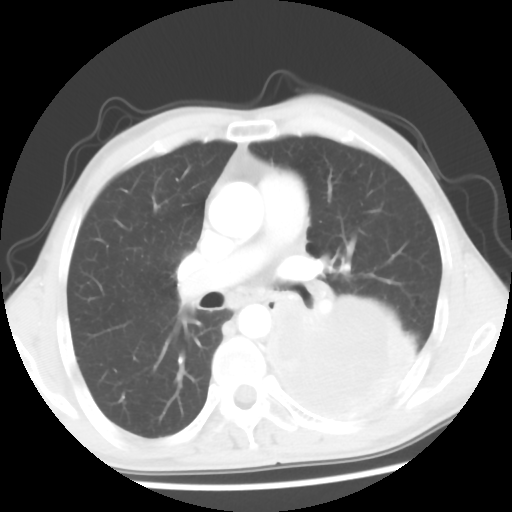
Chest CT, one axial slice; position 32 of 56 along the scan axis; 120 kVp; lung window (W 1500 / L -600 HU); 5 mm slice thickness; 512 × 512 image matrix. Patient: male, 60 years. Case-level facts recorded for this patient, not image findings: clinical TNM (as recorded): T4 N0 M0.
Annotated regions visible in this slice (rectangle marked by the reading radiologist):
- lung tumour (recorded histology: squamous cell carcinoma): bounding box [x1, y1, x2, y2] px = [251, 277, 431, 465]